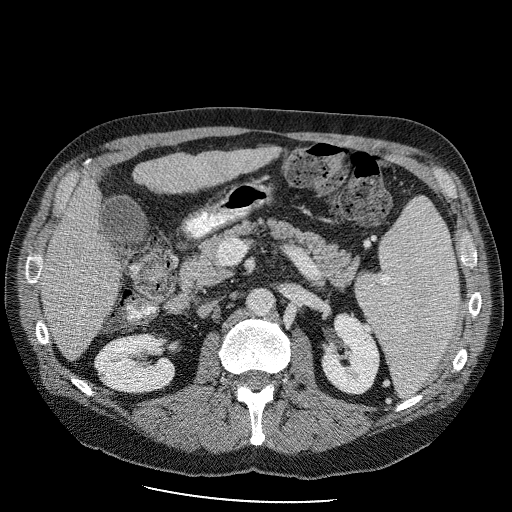
Contrast-enhanced abdominal CT (liver protocol), one axial slice; slice 37 of 98 in the series (ordered by position); 120 kVp; soft-tissue window (W 400 / L 40 HU); 2.5 mm slice thickness; 512 × 512 image matrix, field of view 400 × 400 mm. From the clinical record (not read from this slice): diagnosis: hepatocellular carcinoma (patient treated with transarterial chemoembolisation; whether this scan precedes or follows treatment is not stated here); TNM stage (as recorded): Stage-II; Child-Pugh class: B; tumour nodularity: uninodular.
Structures marked on this image (semi-automatic segmentation, software-assisted and operator-edited):
- liver parenchyma outside the tumour (the mass and vessels are separate outlines, so this box may not span the whole liver): bounding box (x1, y1, x2, y2) in pixels: (39, 142, 286, 356)